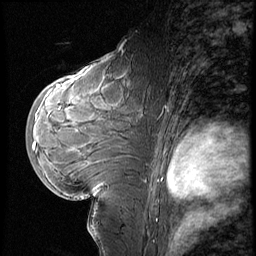
Breast MRI (dynamic contrast-enhanced), one sagittal slice; slice 37 of 60 in the series (ordered by position); 3 images stored at this slice position (order not interpretable as contrast timing); 1.5 T; TE 4.2 ms, TR 8.9 ms; 2.5 mm slice thickness; 256 × 256 image matrix. Female patient, age 29 years. Case-level facts recorded for this patient, not image findings: setting: breast cancer imaged before/during neoadjuvant chemotherapy.
Structures marked on this image (semi-automatic segmentation, software-assisted and operator-edited):
- analysis volume of interest (the breast-tissue region the enhancement analysis was run in; not a lesion): bounding box [x1, y1, x2, y2] px = [29, 57, 150, 200]
- tumour enhancement mask (voxels above the 140 % enhancement threshold inside the analysis volume of interest): [35, 86, 60, 145]